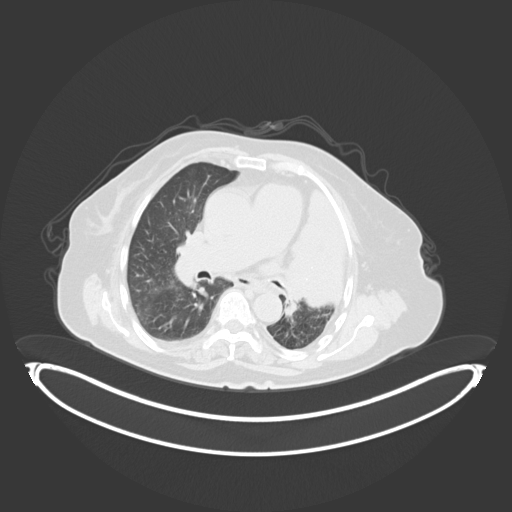
Chest CT, one axial slice. Slice 201 of 284 in the series (ordered by position). Lung window (W 1500 / L -600 HU). 3 mm slice thickness. 512 × 512 image matrix. Patient: female, 75 years. From the clinical record (not read from this slice): clinical TNM (as recorded): T3 N3 M1.
Outlined on this slice (bounding box drawn by a radiologist):
- lung tumour (recorded histology: adenocarcinoma): bounding box (x1, y1, x2, y2) in pixels: (279, 191, 354, 310)